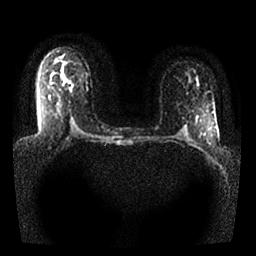
Breast MRI, one axial slice. Position 19 of 25 along the scan axis. Diffusion-weighted series; image 2 of 4 stored at this slice position (different b-values; order by instance number). 1.5 T. 256 × 256 image matrix. Female patient.
Annotated regions visible in this slice (expert manual segmentation):
- tumour on diffusion-weighted imaging: bounding box <69,88,72,91> (left, top, right, bottom; pixels)